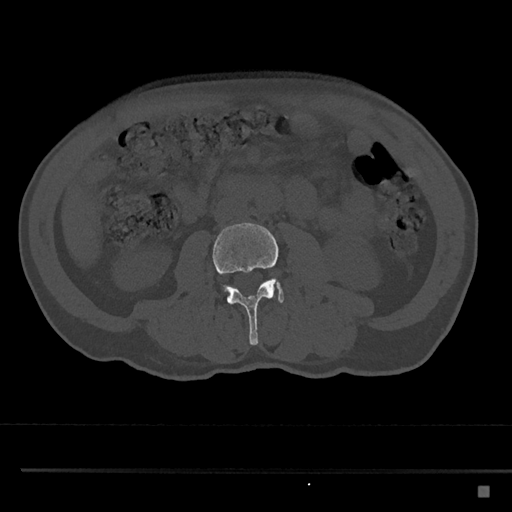
CT including the spine, one axial slice; position 688 of 797 along the scan axis; bone window (W 1800 / L 400 HU); 512 × 512 image matrix, field of view 391 × 391 mm. Patient: male, 59 years. From the clinical record (not read from this slice): primary cancer: prostate.
Annotated regions visible in this slice (semi-automatically segmented with operator editing):
- L3 vertebra: bounding box [x1, y1, x2, y2] px = [212, 222, 279, 345]
- L4 vertebra: [224, 279, 284, 303]